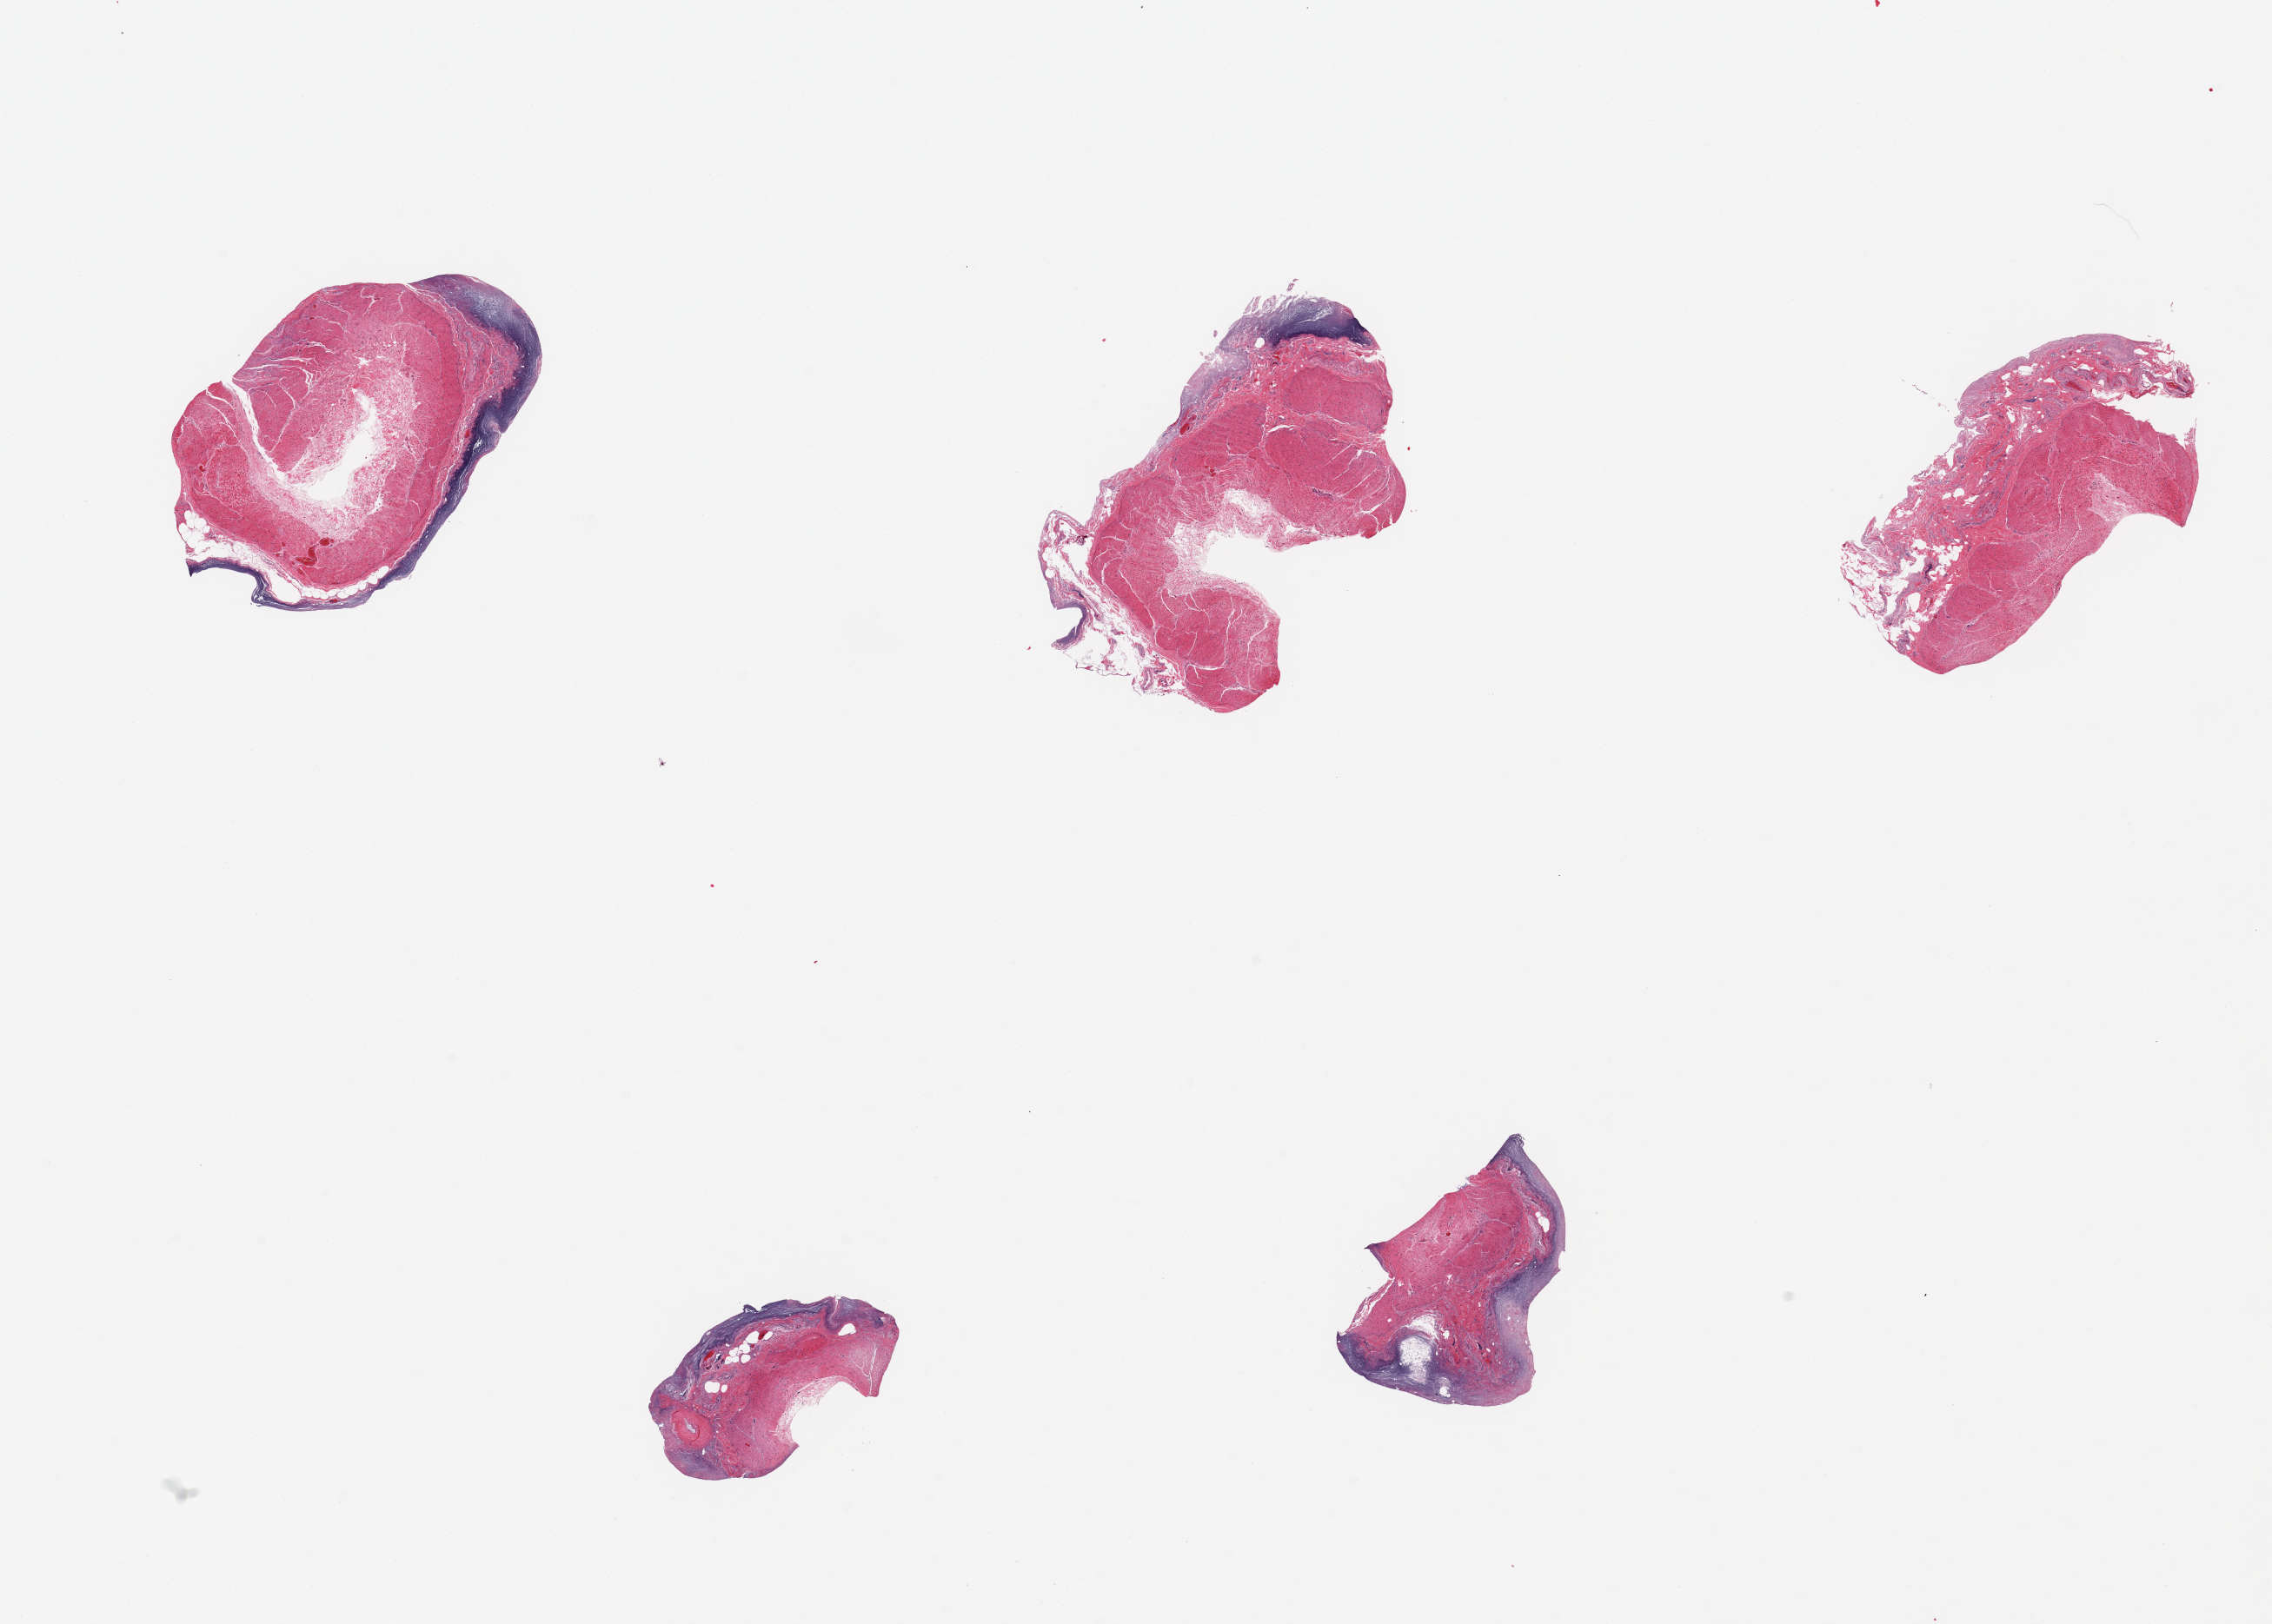
Digitized H&E-stained section, brightfield, whole scanned area (about 20.7 x 14.8 mm) shown as a low-resolution overview; PAXgene-fixed paraffin-embedded (PFPE) section; sampled site (target tissue): ileum; tissue donor sample. Donor: male.
Pathologist's review note for this sample: 5 pieces; autolyzed, also includes muscularis (not target).